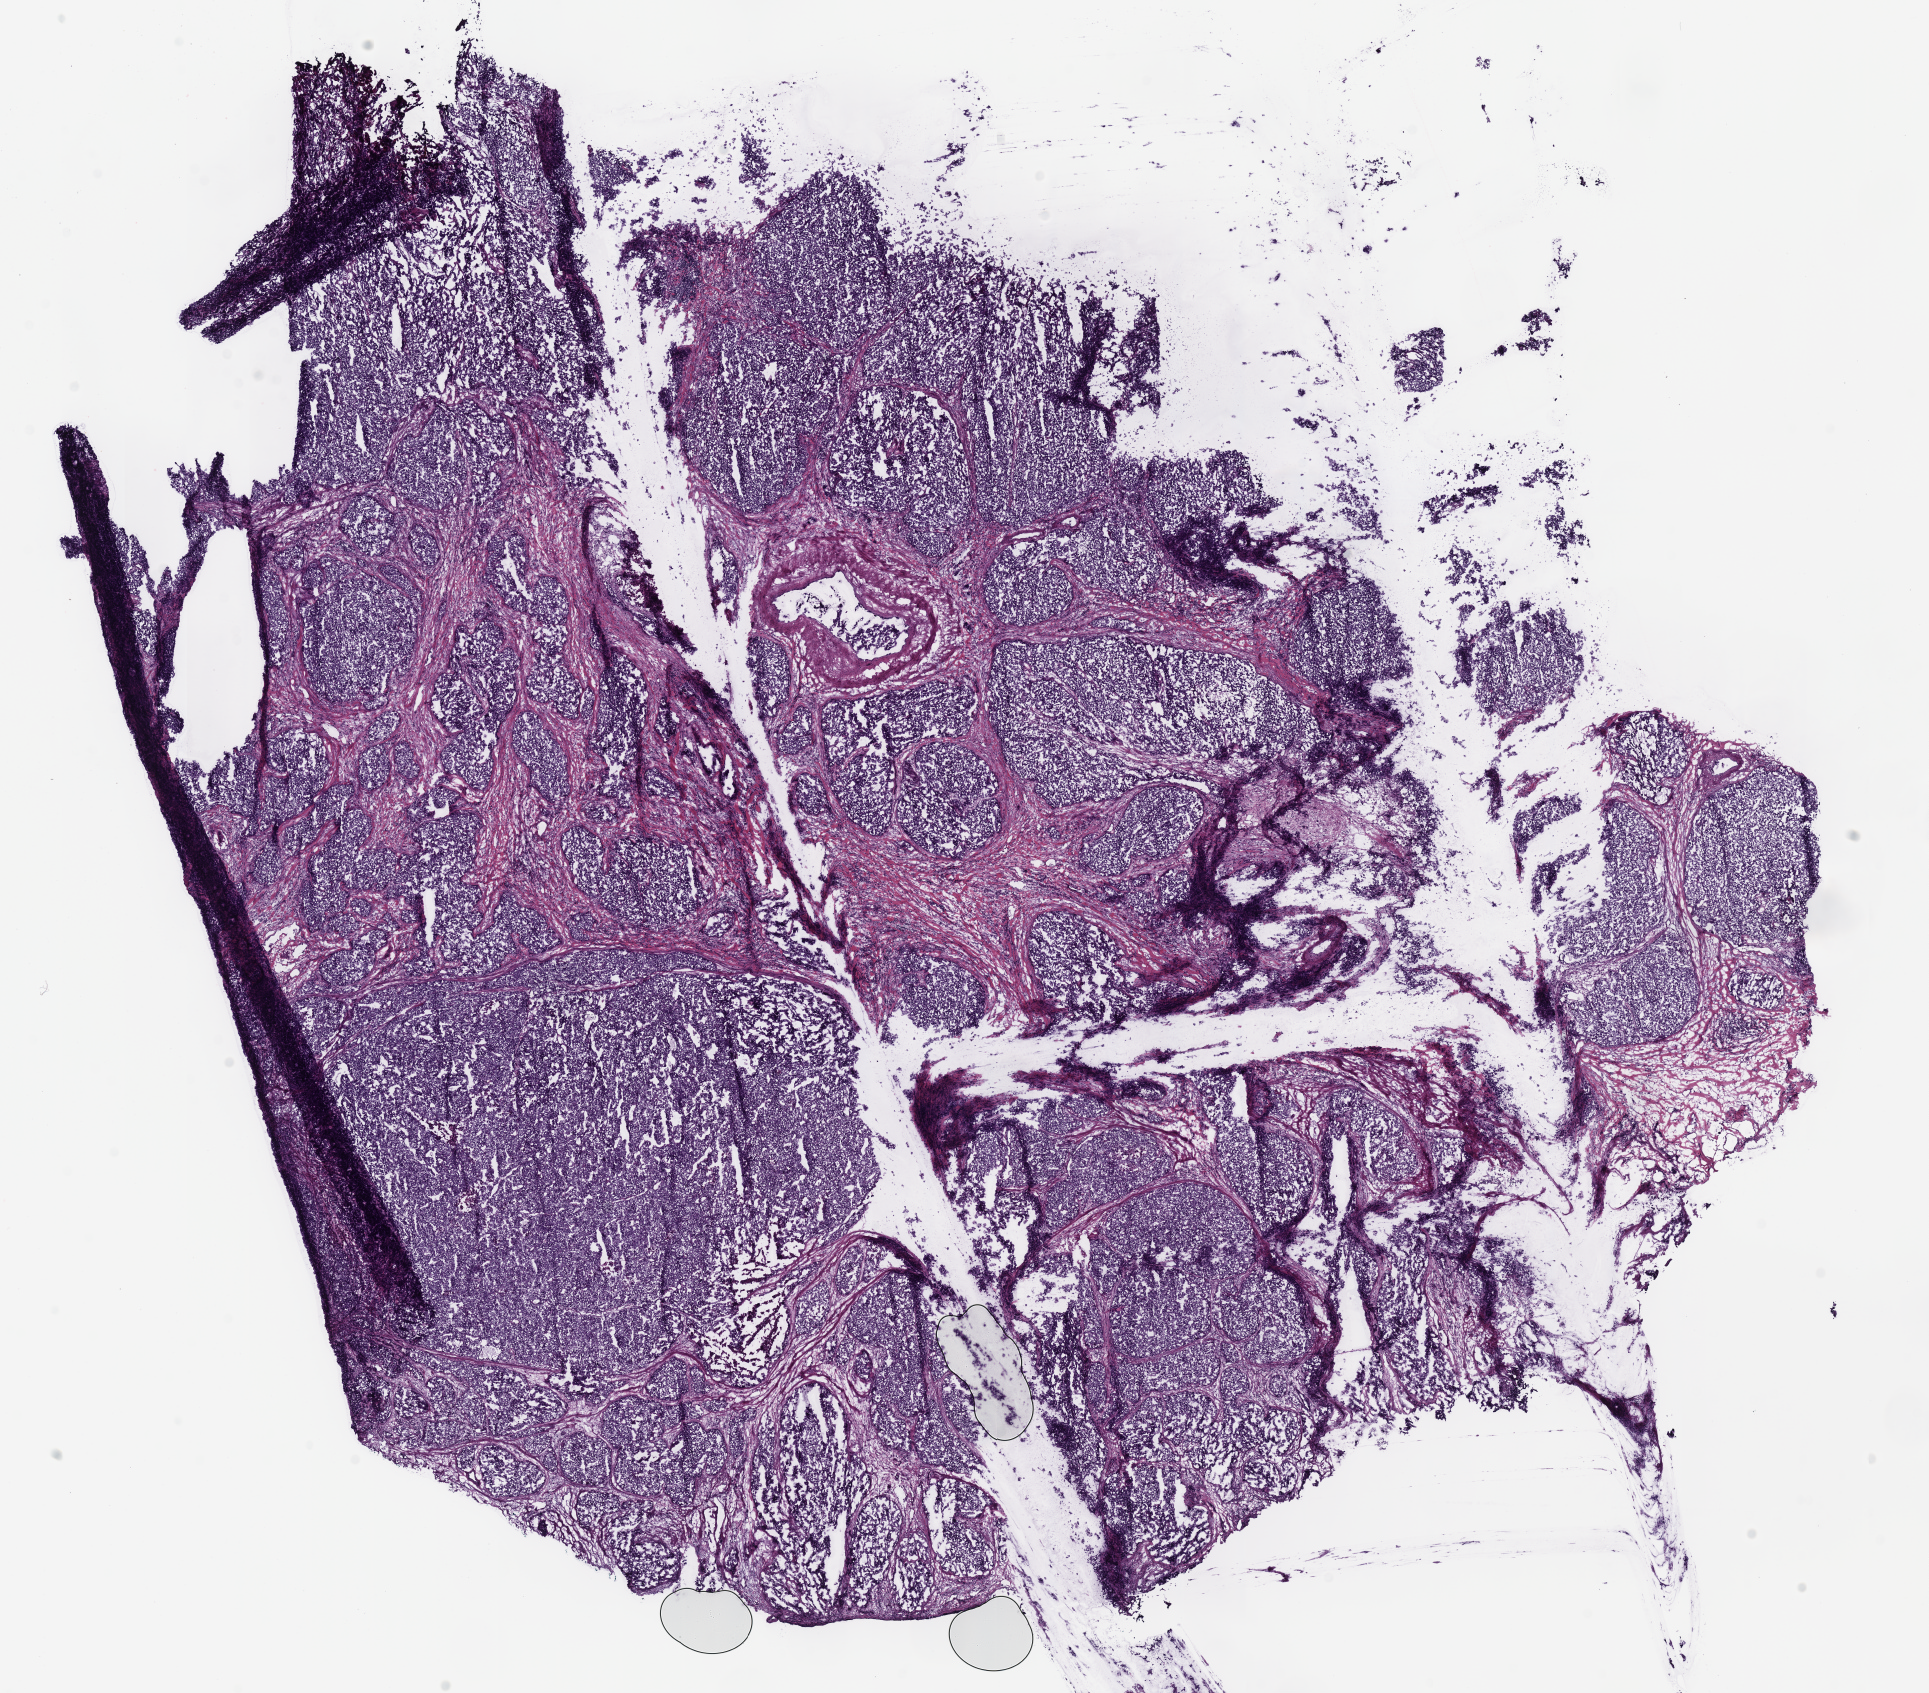
Whole-slide histology image, H&E-stained, a low-resolution overview of the entire scanned area, about 15.2 x 13.3 mm (acquisition: 40x scan). Frozen section from the bottom of the tissue portion. Primary tumour sample from the stomach. Patient: female, age at initial diagnosis 60 years. Histologic grade: G3 (poorly differentiated). Composition of this section per pathologist review: tumour cells 85%, tumour nuclei 85%, normal cells 0%, stromal cells 15%, necrosis 0%.
Histologic diagnosis: Adenocarcinoma, intestinal type (body of stomach). AJCC pathologic stage: IIB (7th edition).